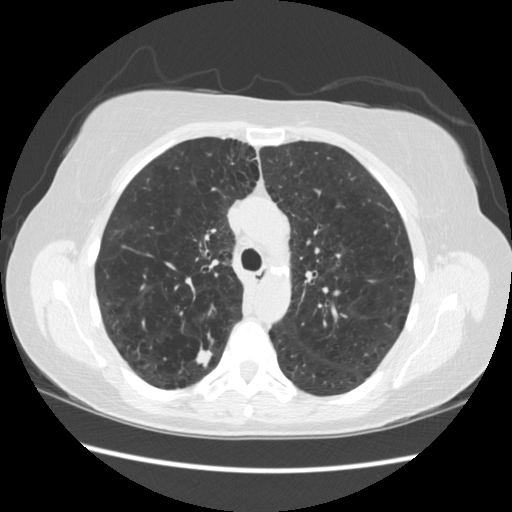
Low-dose screening chest CT, one axial slice. Position 163 of 235 along the scan axis. 120 kVp. Lung window (W 1500 / L -600 HU). 2.5 mm slice thickness. 512 × 512 image matrix.
Structures marked on this image (manually delineated by an expert):
- lesion 1 (tumor, upper lobe of right lung): bounding box <195,346,214,367> (left, top, right, bottom; pixels)